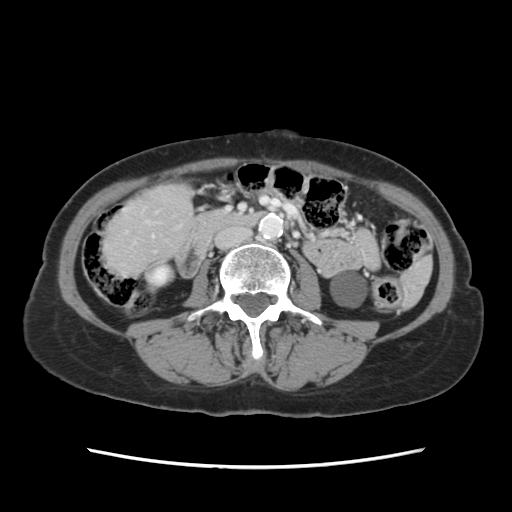
Contrast-enhanced abdominal CT, one axial slice; position 20 of 120 along the scan axis; 120 kVp; intravenous contrast given; soft-tissue window (W 400 / L 40 HU); 512 × 512 image matrix. Female patient, age 70 years. From the clinical record (not read from this slice): diagnosis: colorectal cancer liver metastases, imaged before liver resection; multiple liver metastases: no; largest metastasis: 2.5 cm; chemotherapy before resection: yes.
Annotated regions visible in this slice (expert manual segmentation):
- liver: box from (x=105, y=185) to (x=191, y=274) px
- planned liver remnant (the part of the liver to remain after resection): (x=104, y=185)–(x=191, y=273)